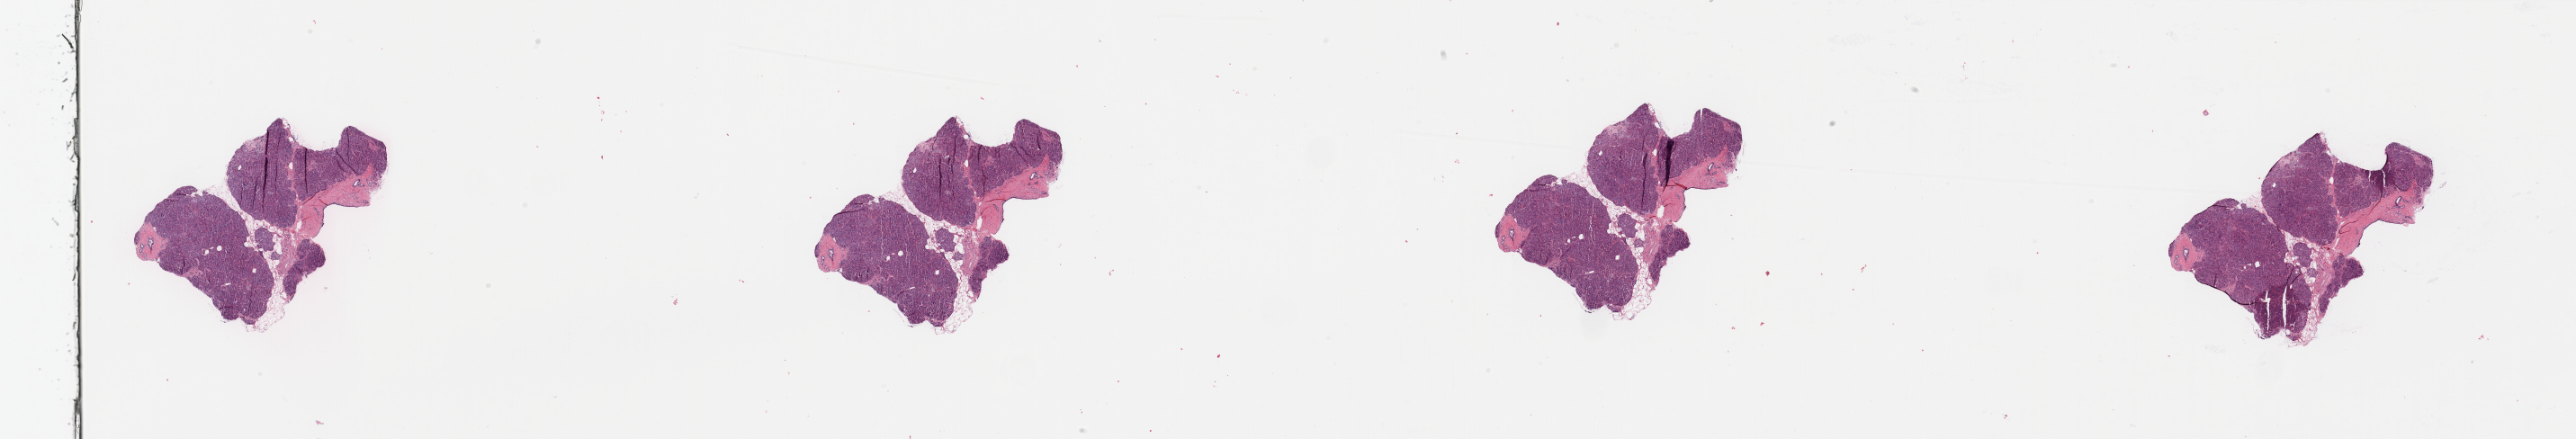
H&E-stained whole-slide image, a low-resolution overview of the entire scanned area, about 45.3 x 7.7 mm (from a 20x scan), pancreas, normal (non-tumour) tissue. Patient: male, age 78 years.
This section: normal (non-tumour) tissue from the same patient. Patient diagnosis: Infiltrating duct carcinoma, NOS.